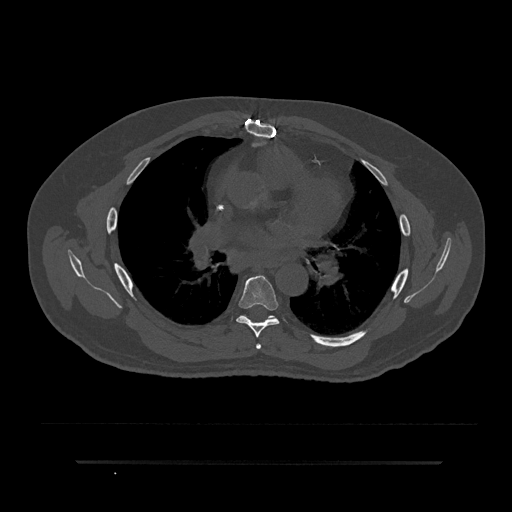
CT including the spine, one axial slice. Position 520 of 797 along the scan axis. Reconstruction kernel Br40s/3. Bone window (W 1800 / L 400 HU). 512 × 512 image matrix, field of view 464 × 464 mm. Male patient, age 59 years. From the clinical record (not read from this slice): primary cancer: bile ducts.
Structures marked on this image (semi-automatically segmented with operator editing):
- T5 vertebra: bounding box (x1, y1, x2, y2) in pixels: (256, 343, 261, 349)
- T6 vertebra: (236, 276, 280, 338)